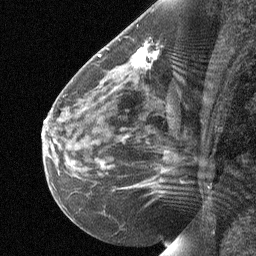
Breast MRI (dynamic contrast-enhanced), one sagittal slice. Slice 34 of 64 in the series (ordered by position). Dynamic contrast-enhanced study with each time point stored as its own series, time point 2 of 3 at this slice position (early post-contrast, ordered by acquisition time). 1.5 T. TE 4.8 ms, TR 27 ms. 2 mm slice thickness. 256 × 256 image matrix, field of view 180 × 180 mm. Female patient, age 51 years. From the clinical record (not read from this slice): setting: breast cancer imaged before/during neoadjuvant chemotherapy; receptor status: HR-positive, HER2-negative.
Annotated regions visible in this slice (semi-automatic segmentation, software-assisted and operator-edited):
- analysis volume of interest (the breast-tissue region the enhancement analysis was run in; not a lesion): box from (x=81, y=35) to (x=179, y=103) px
- tumour enhancement mask (voxels above the 90 % enhancement threshold inside the analysis volume of interest): (x=134, y=44)–(x=157, y=65)